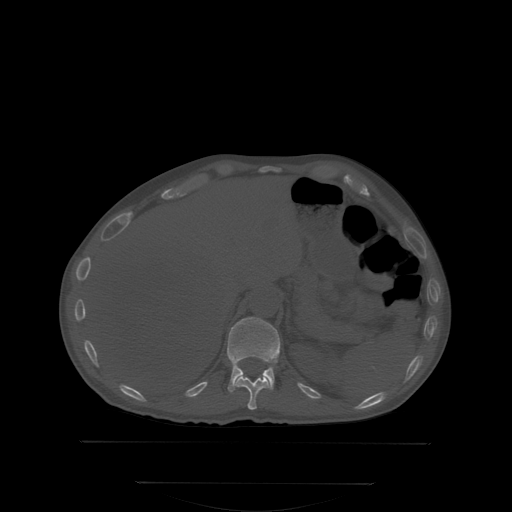
CT including the spine, one axial slice. Position 174 of 350 along the scan axis. Bone window (W 1800 / L 400 HU). 2.5 mm slice thickness. 512 × 512 image matrix, field of view 500 × 500 mm. Patient: male, 58 years. From the clinical record (not read from this slice): primary cancer: prostate.
Annotated regions visible in this slice (semi-automatically segmented with operator editing):
- T11 vertebra: bounding box (x1, y1, x2, y2) in pixels: (236, 376, 267, 409)
- T12 vertebra: (228, 317, 279, 390)